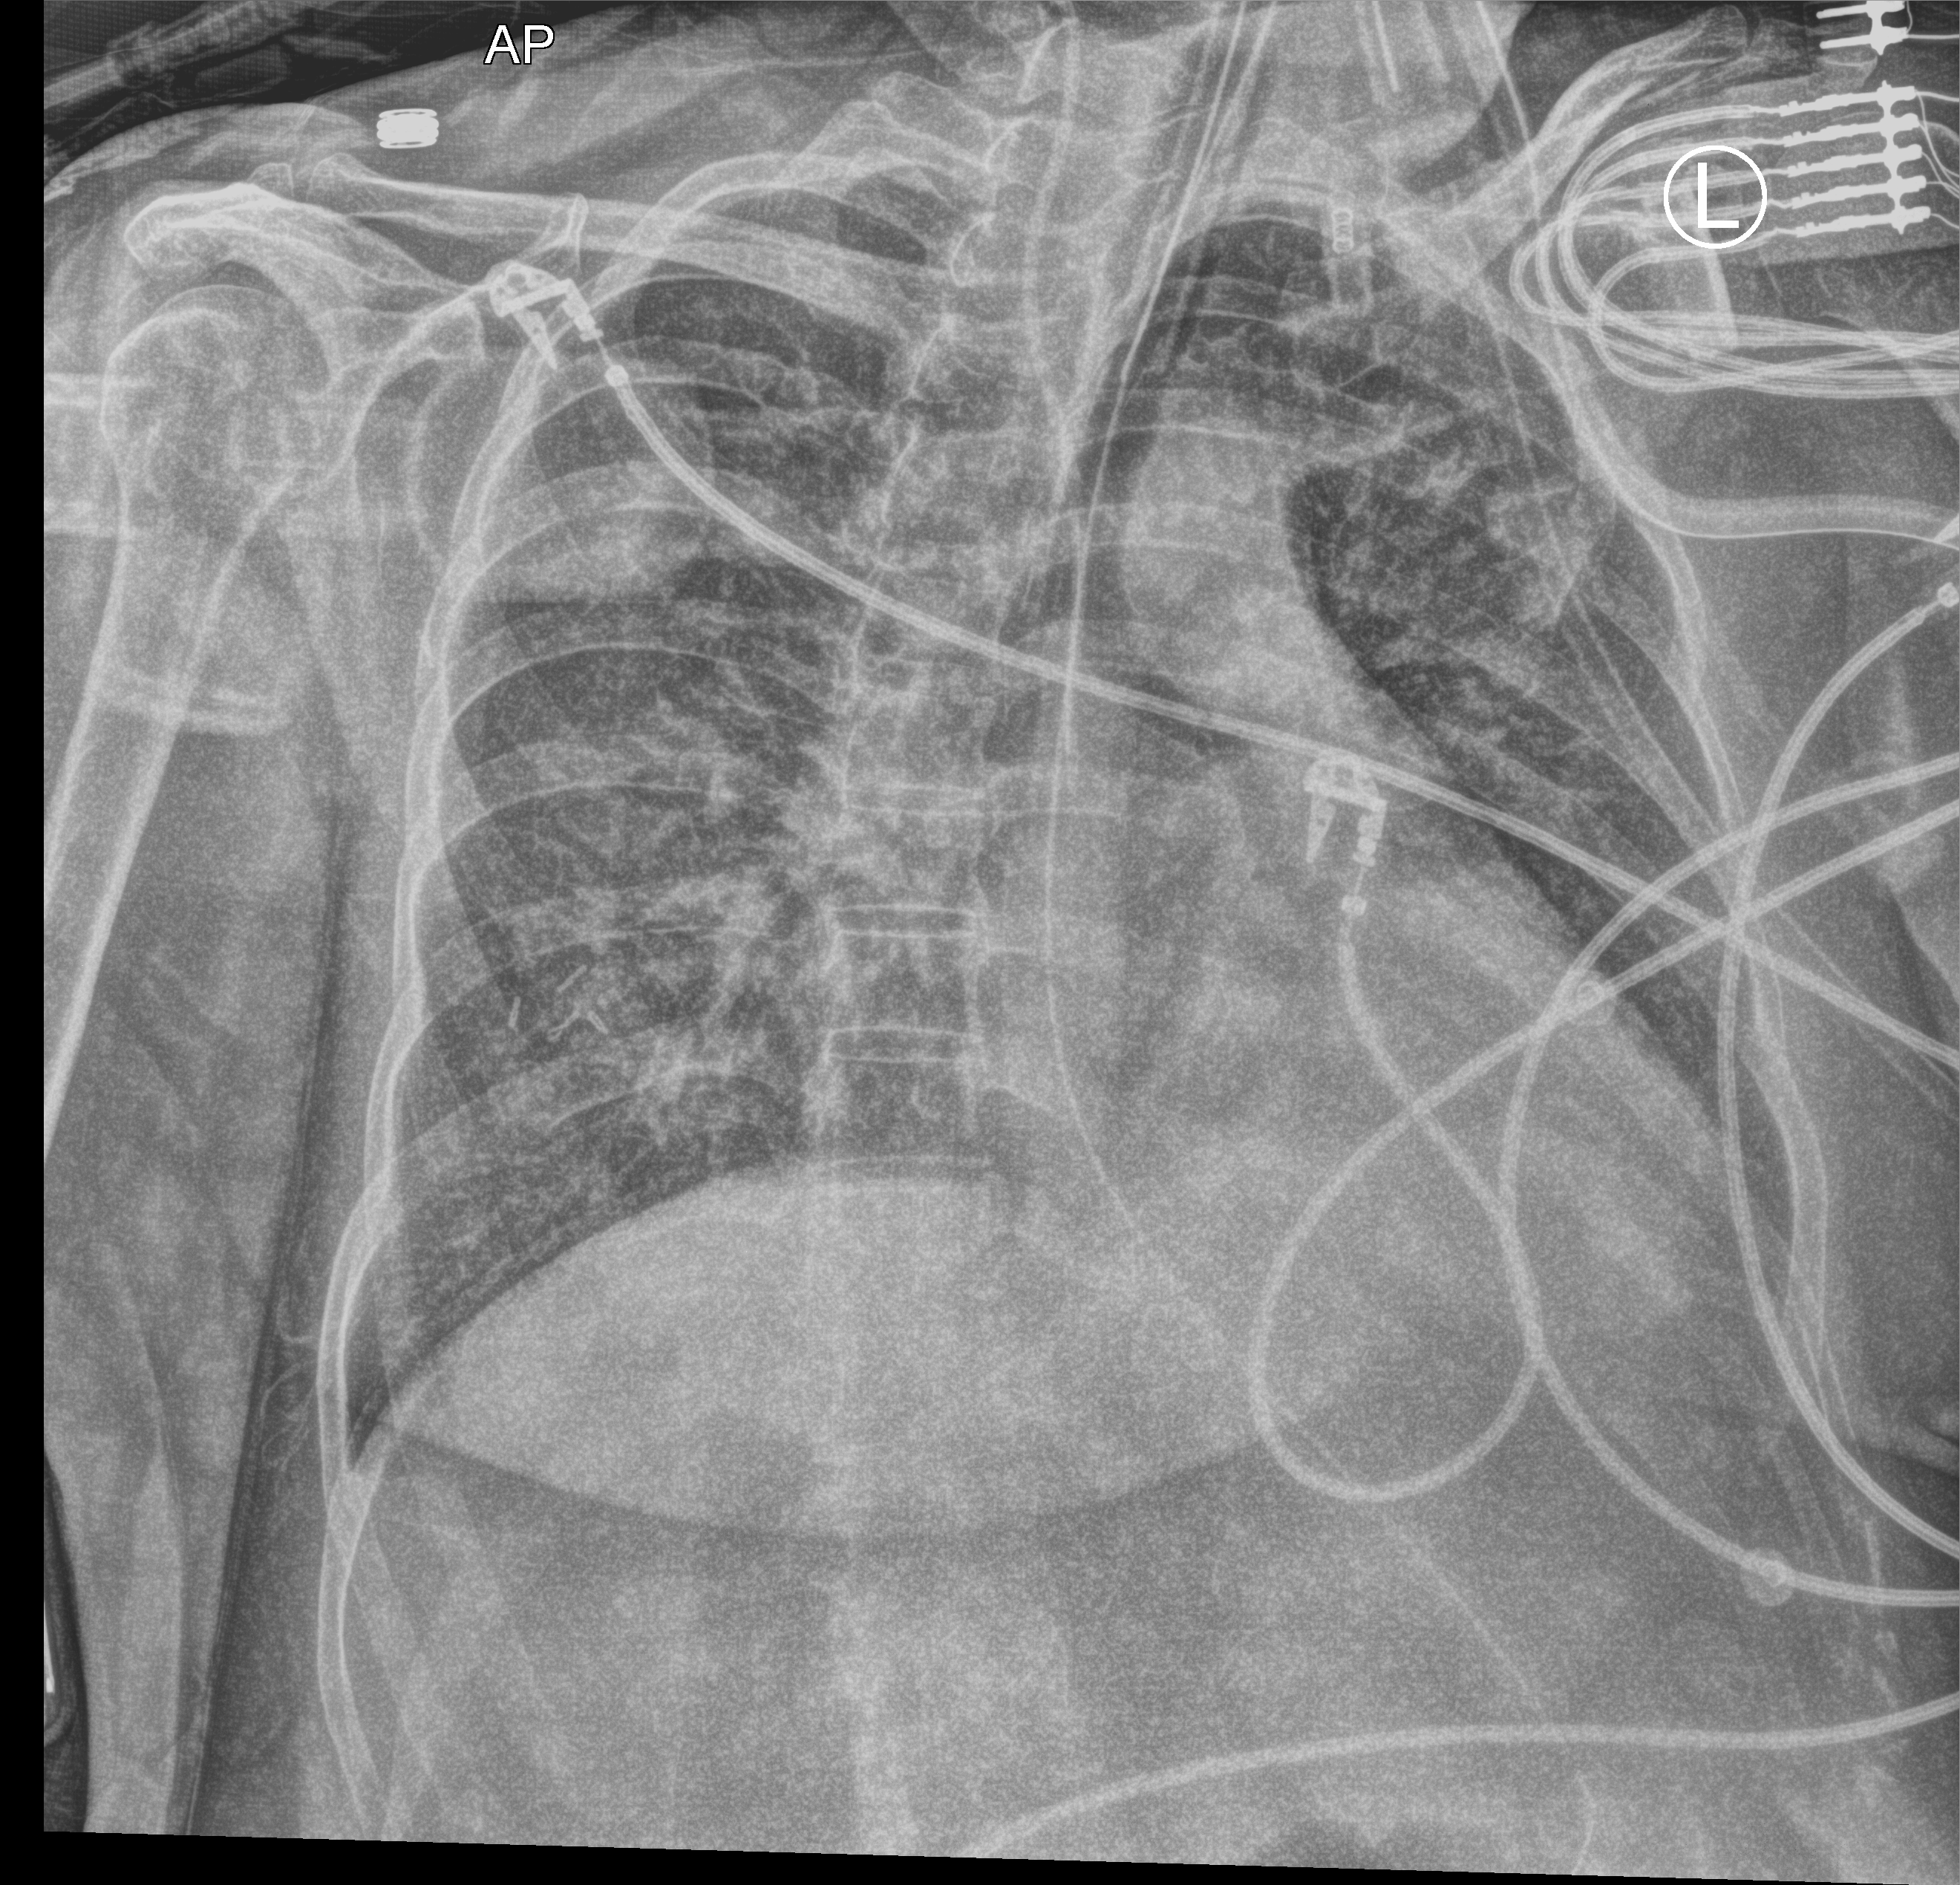
Portable chest radiograph, anteroposterior (AP) projection. Patient hospitalised with COVID-19; female, aged 18–59 years.
Hospital-stay facts (about this admission, not read from this image; timing relative to this image not recorded): mechanically ventilated during this hospital stay: yes; admitted to intensive care during this hospital stay: no; COPD (admission record): no.